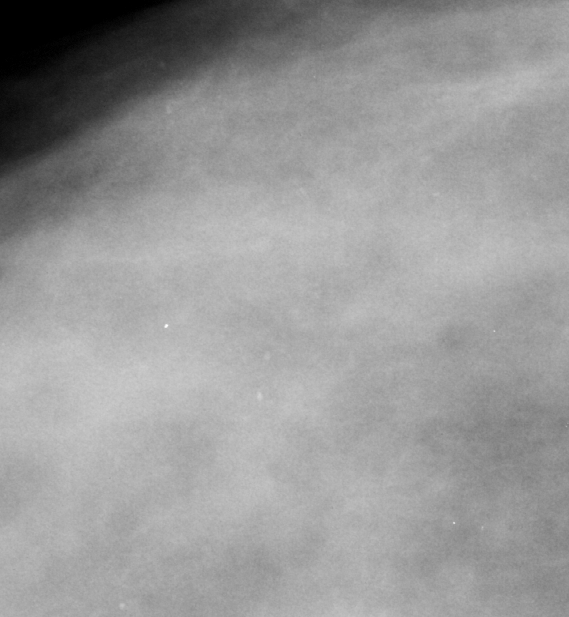
Region of interest cut from a scanned film mammogram (one marked finding); right breast; CC view; BI-RADS breast density category 3 (scale 1–4).
- Calcifications, morphology punctate, distribution clustered; BI-RADS assessment category 3; subtlety rating 2 on a 1 (subtle) to 5 (obvious) scale; pathology result (as recorded, not read from the image): benign.